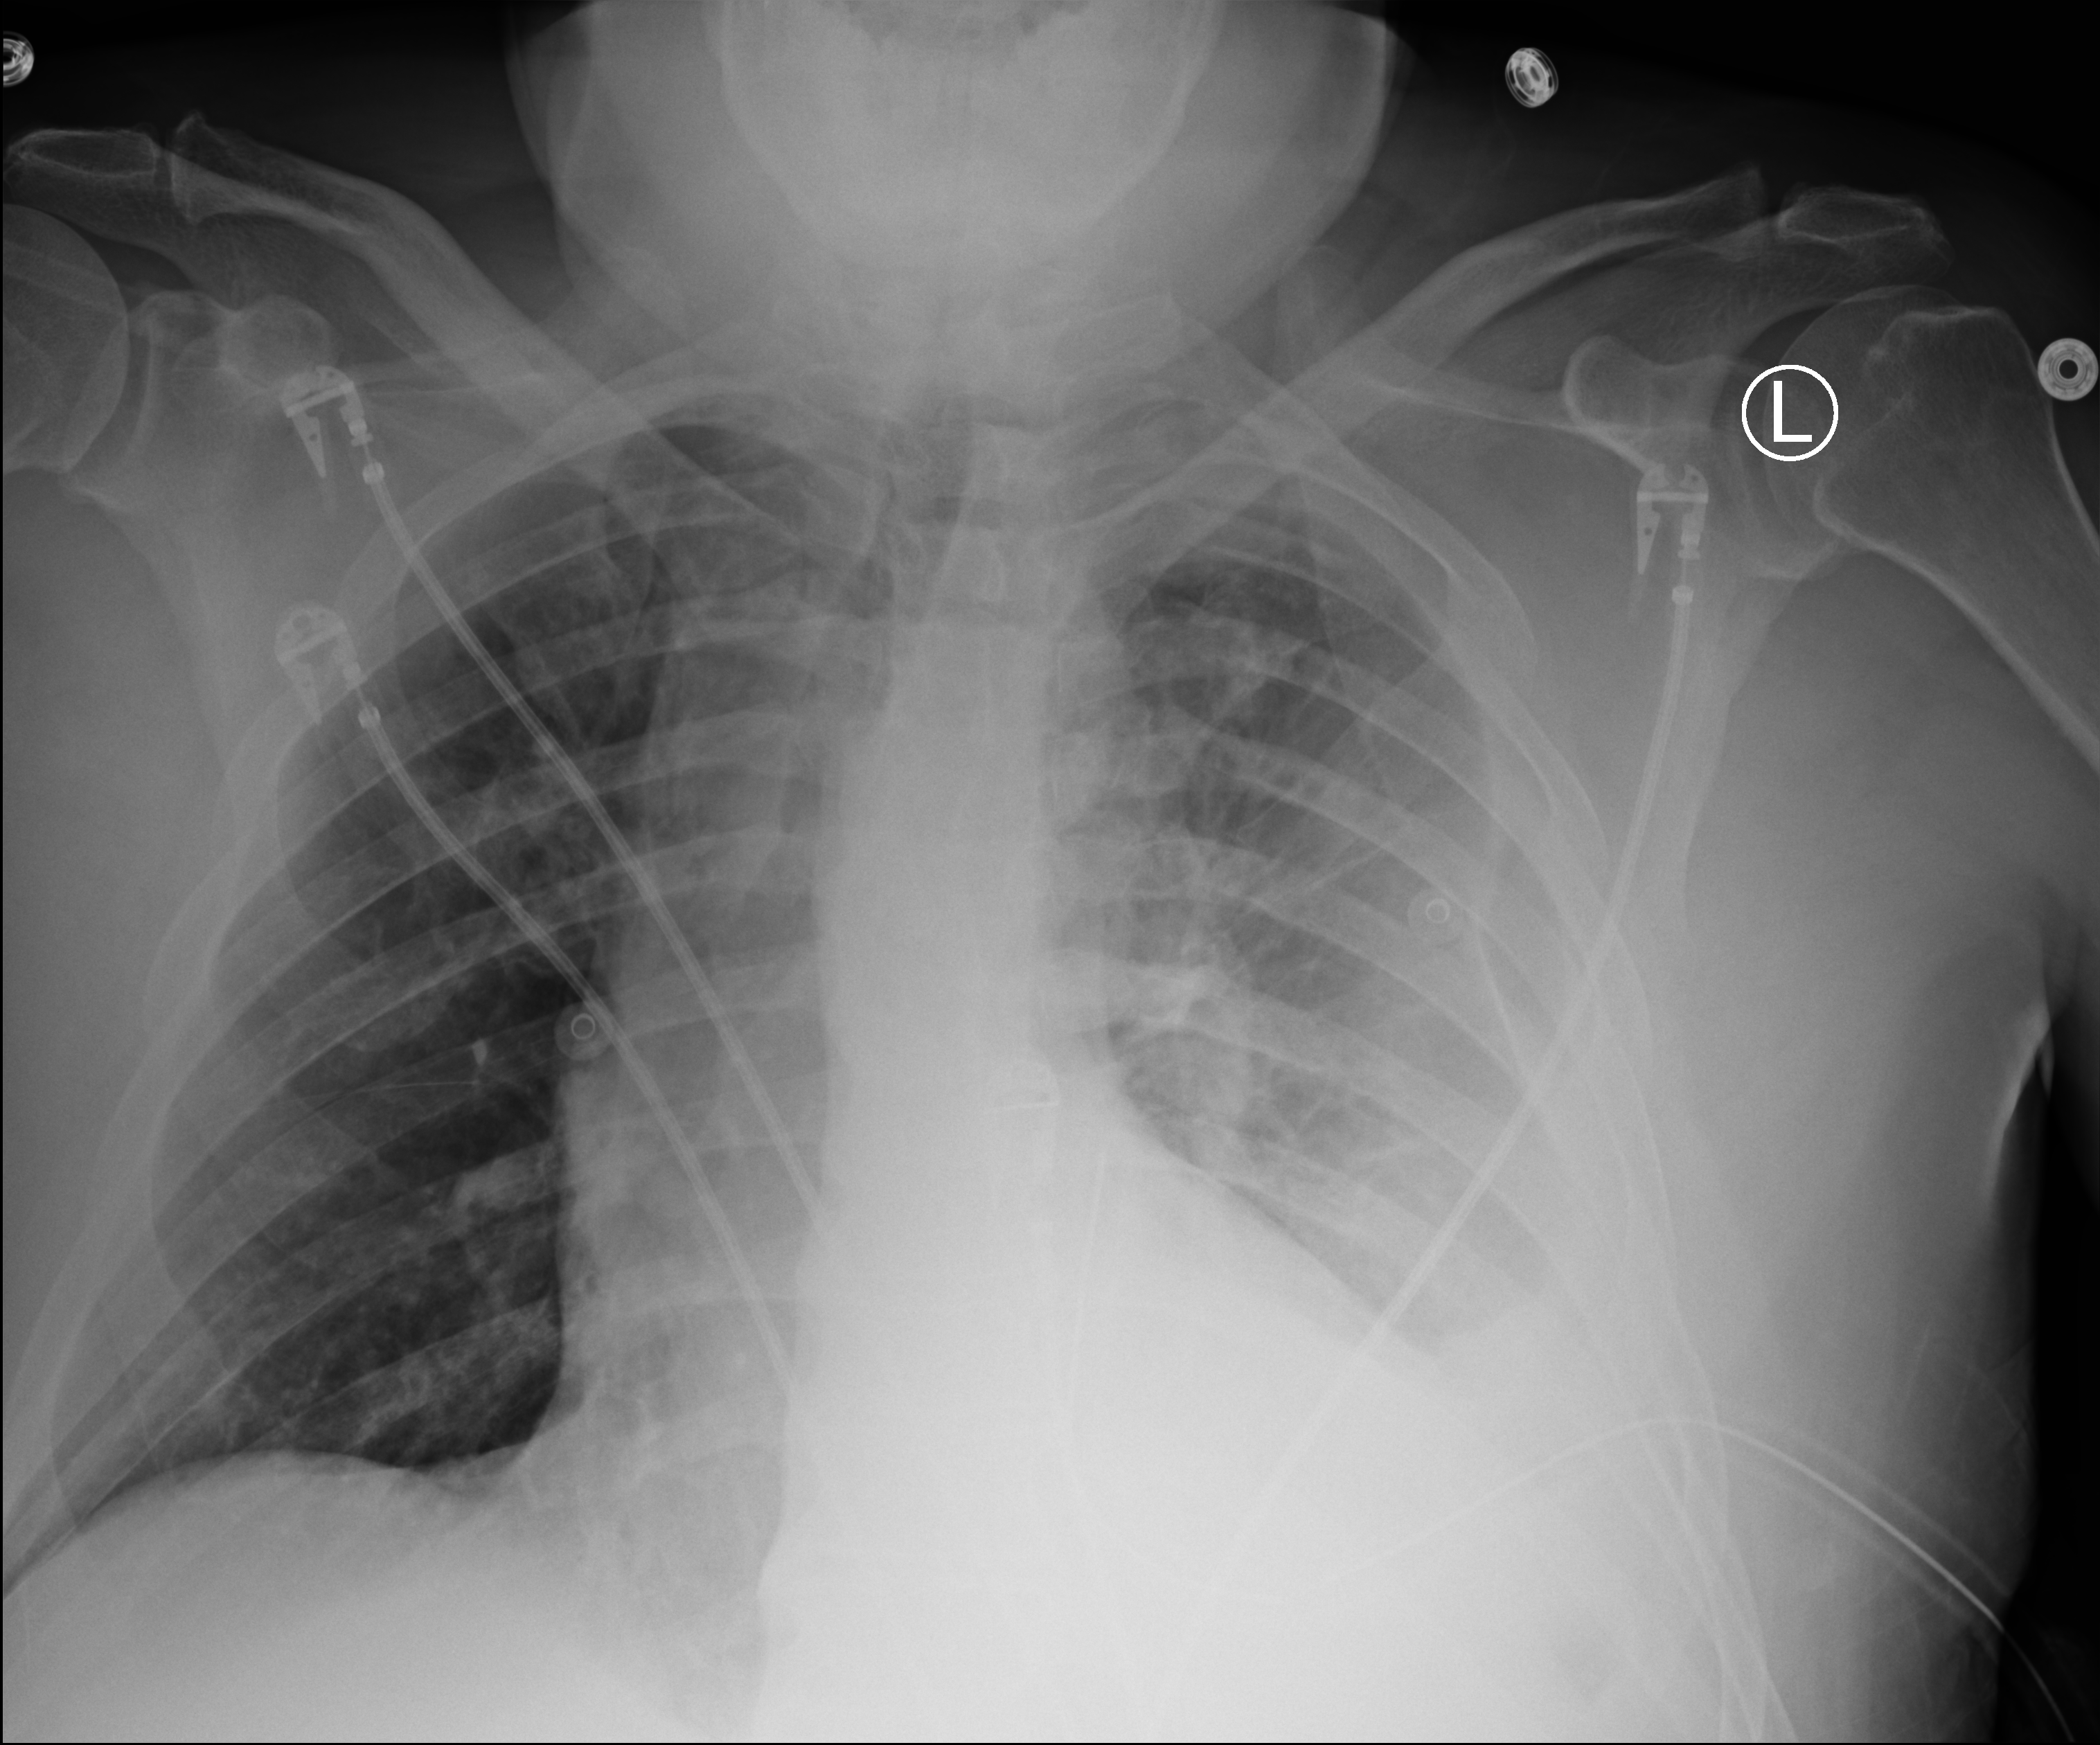
Portable chest radiograph; anteroposterior (AP) projection. Male patient hospitalised with COVID-19, age 18–59 years.
Hospital-stay facts (about this admission, not read from this image; timing relative to this image not recorded):
- mechanically ventilated during this hospital stay: no
- admitted to intensive care during this hospital stay: no